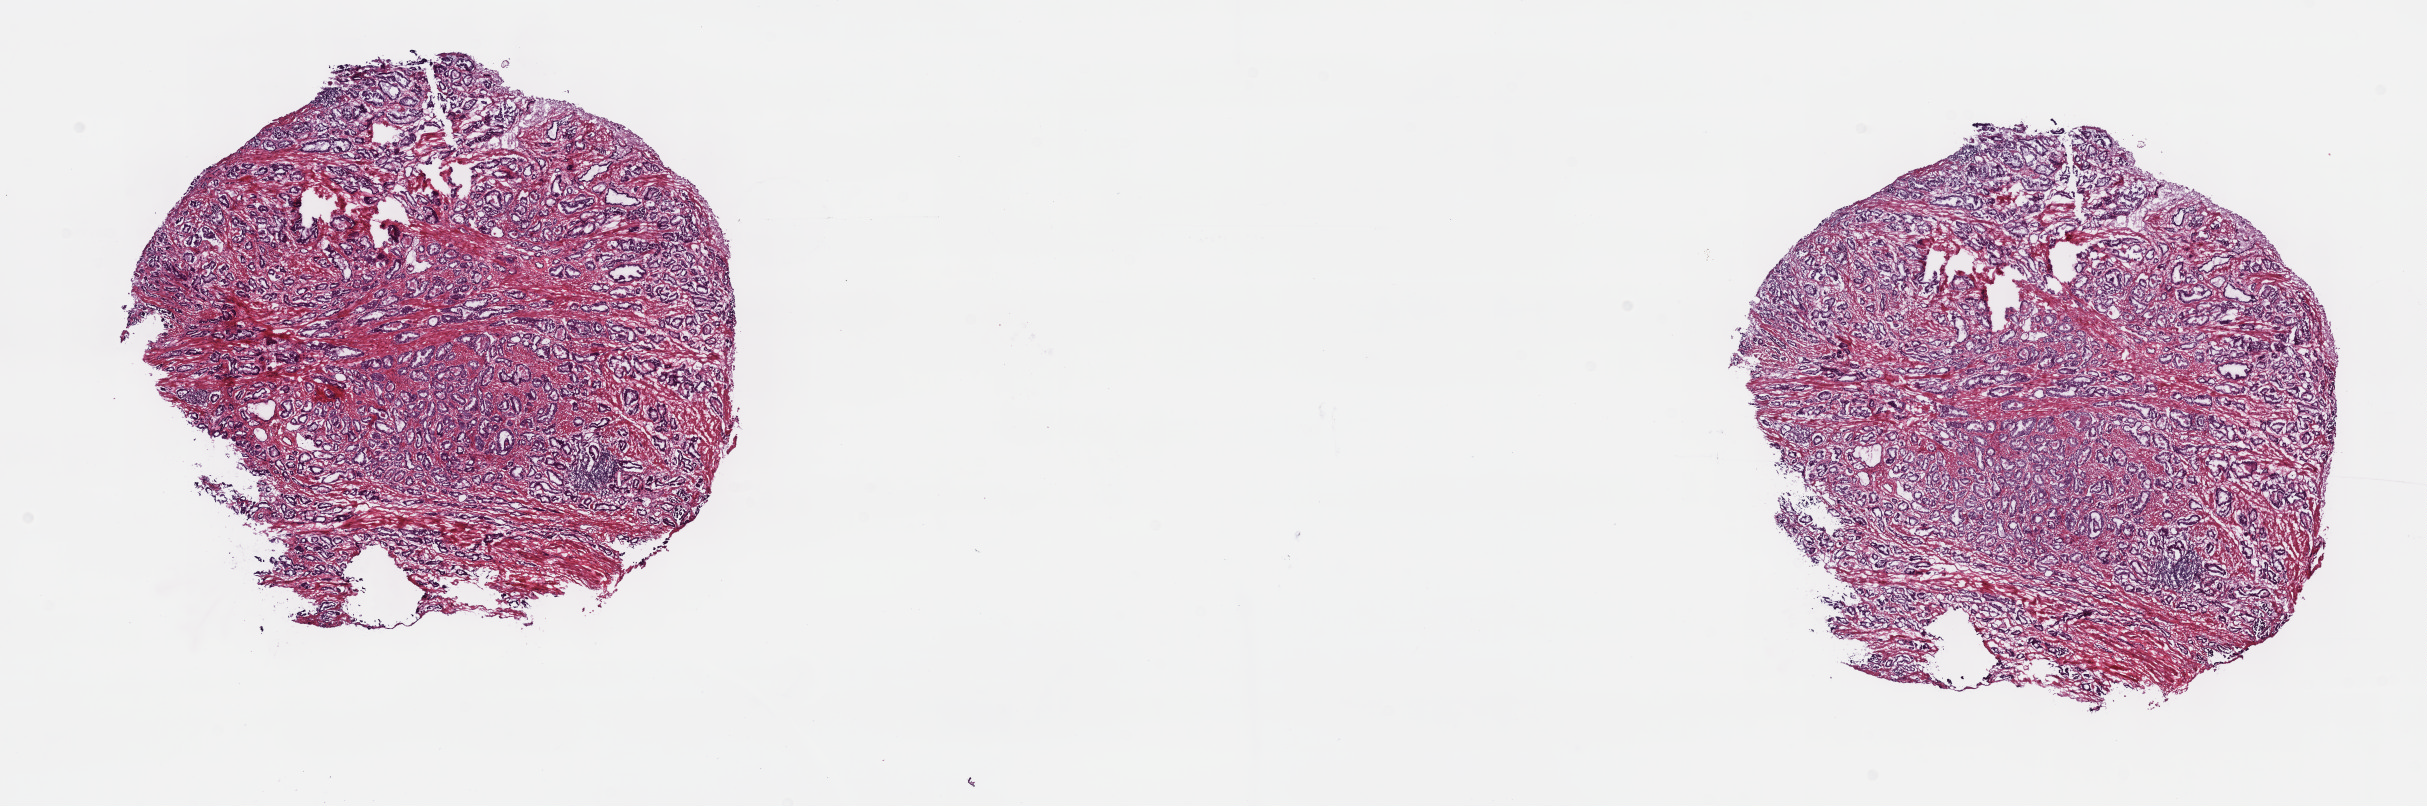
H&E whole-slide image — low-resolution overview of the scanned area, about 19.6 x 6.5 mm (acquisition: 40x scan), frozen section from the top of the tissue portion, primary tumour sample from the prostate. Patient: male, age at initial diagnosis 57 years. Gleason score: 6 (3+3). Slide review estimates, as recorded: tumour cells 55%, tumour nuclei 90%, normal cells 2%, stromal cells 42%, necrosis 1%. Infiltration values recorded for this section: lymphocyte infiltration 7%, monocyte infiltration 0%, neutrophil infiltration 0%.
Pathologic diagnosis: Adenocarcinoma, NOS (prostate gland).